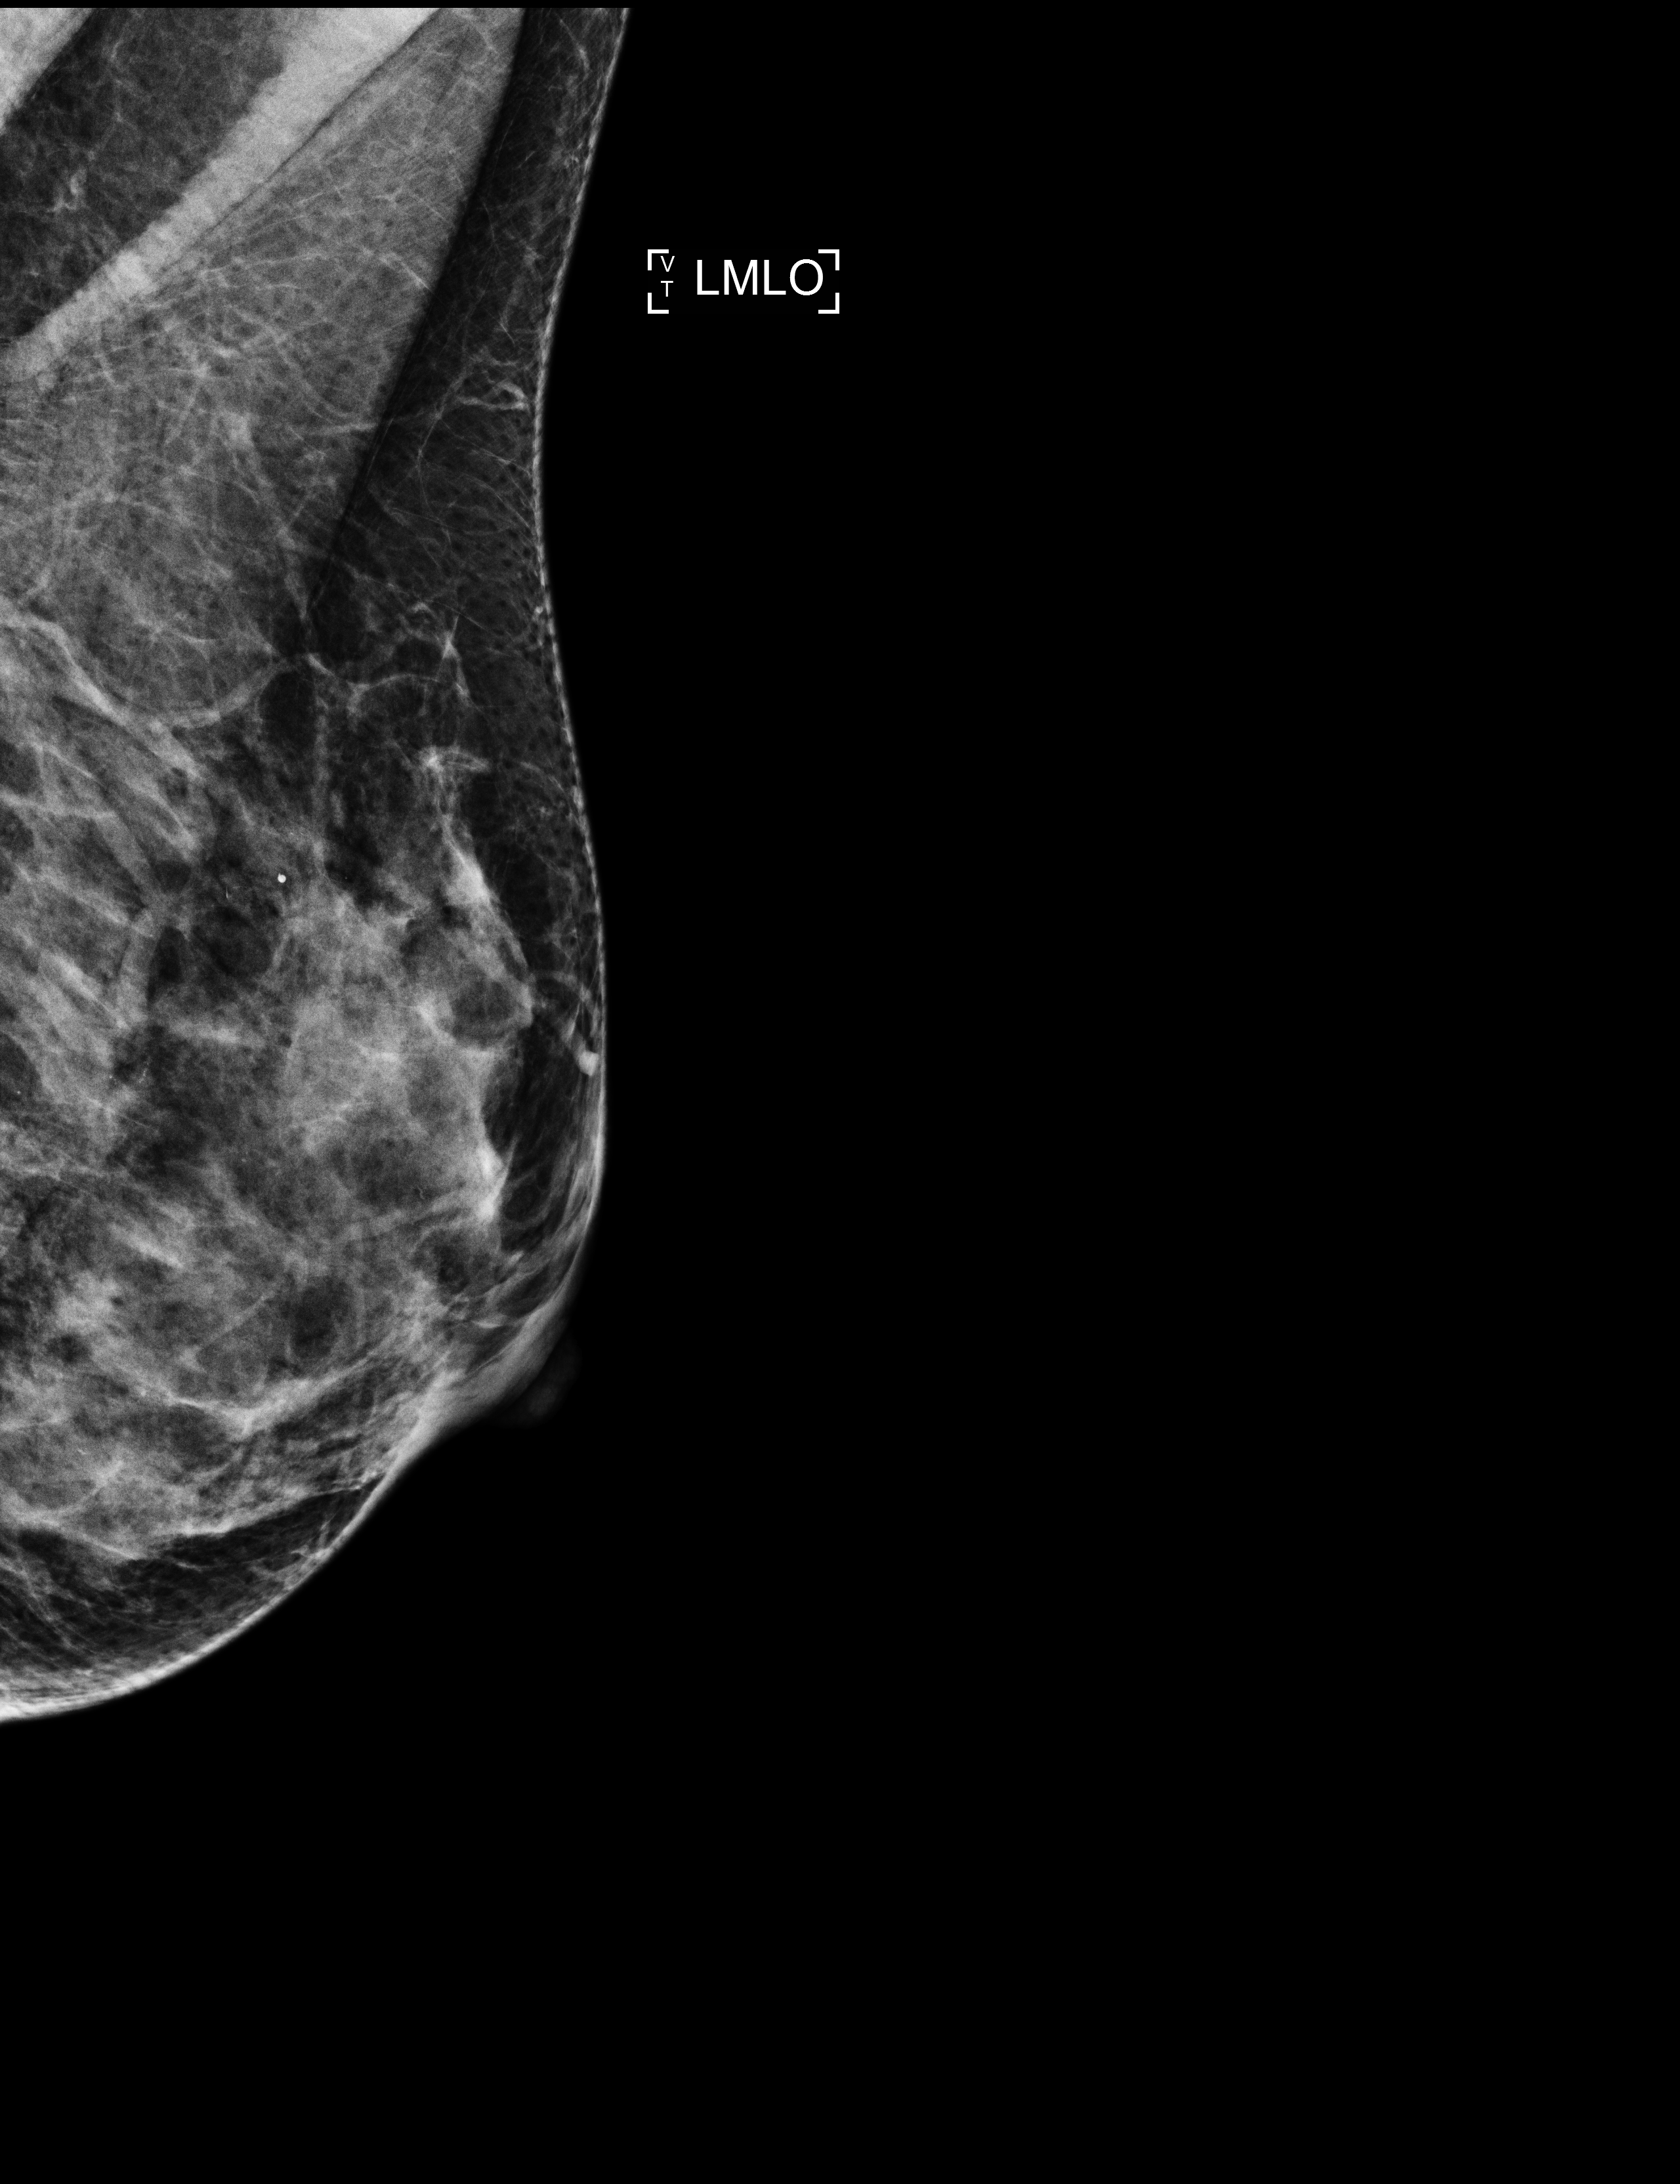
Screening examination, system: Selenia Dimensions. Patient: female, 48 years.
Image type: full-field digital mammogram. Breast: left. Projection: medio-lateral oblique projection.